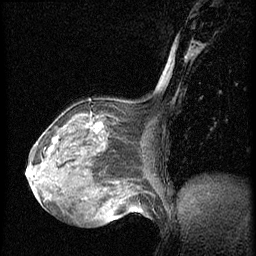
Breast MRI (dynamic contrast-enhanced), one sagittal slice; slice 27 of 56 in the series (ordered by position); dynamic contrast-enhanced series, image 2 of 3 at this slice position (ordered by acquisition); 1.5 T; TE 4.2 ms, TR 20.4 ms; 256 × 256 image matrix, field of view 200 × 200 mm. Female patient, age 64 years. Case-level facts recorded for this patient, not image findings: setting: breast cancer imaged before/during neoadjuvant chemotherapy; receptor status: HR-positive, HER2-negative.
Annotated regions visible in this slice (semi-automatic segmentation, software-assisted and operator-edited):
- analysis volume of interest (the breast-tissue region the enhancement analysis was run in; not a lesion): bounding box (x1, y1, x2, y2) in pixels: (48, 101, 137, 186)
- tumour enhancement mask (voxels above the 70 % enhancement threshold inside the analysis volume of interest): (51, 122, 102, 149)